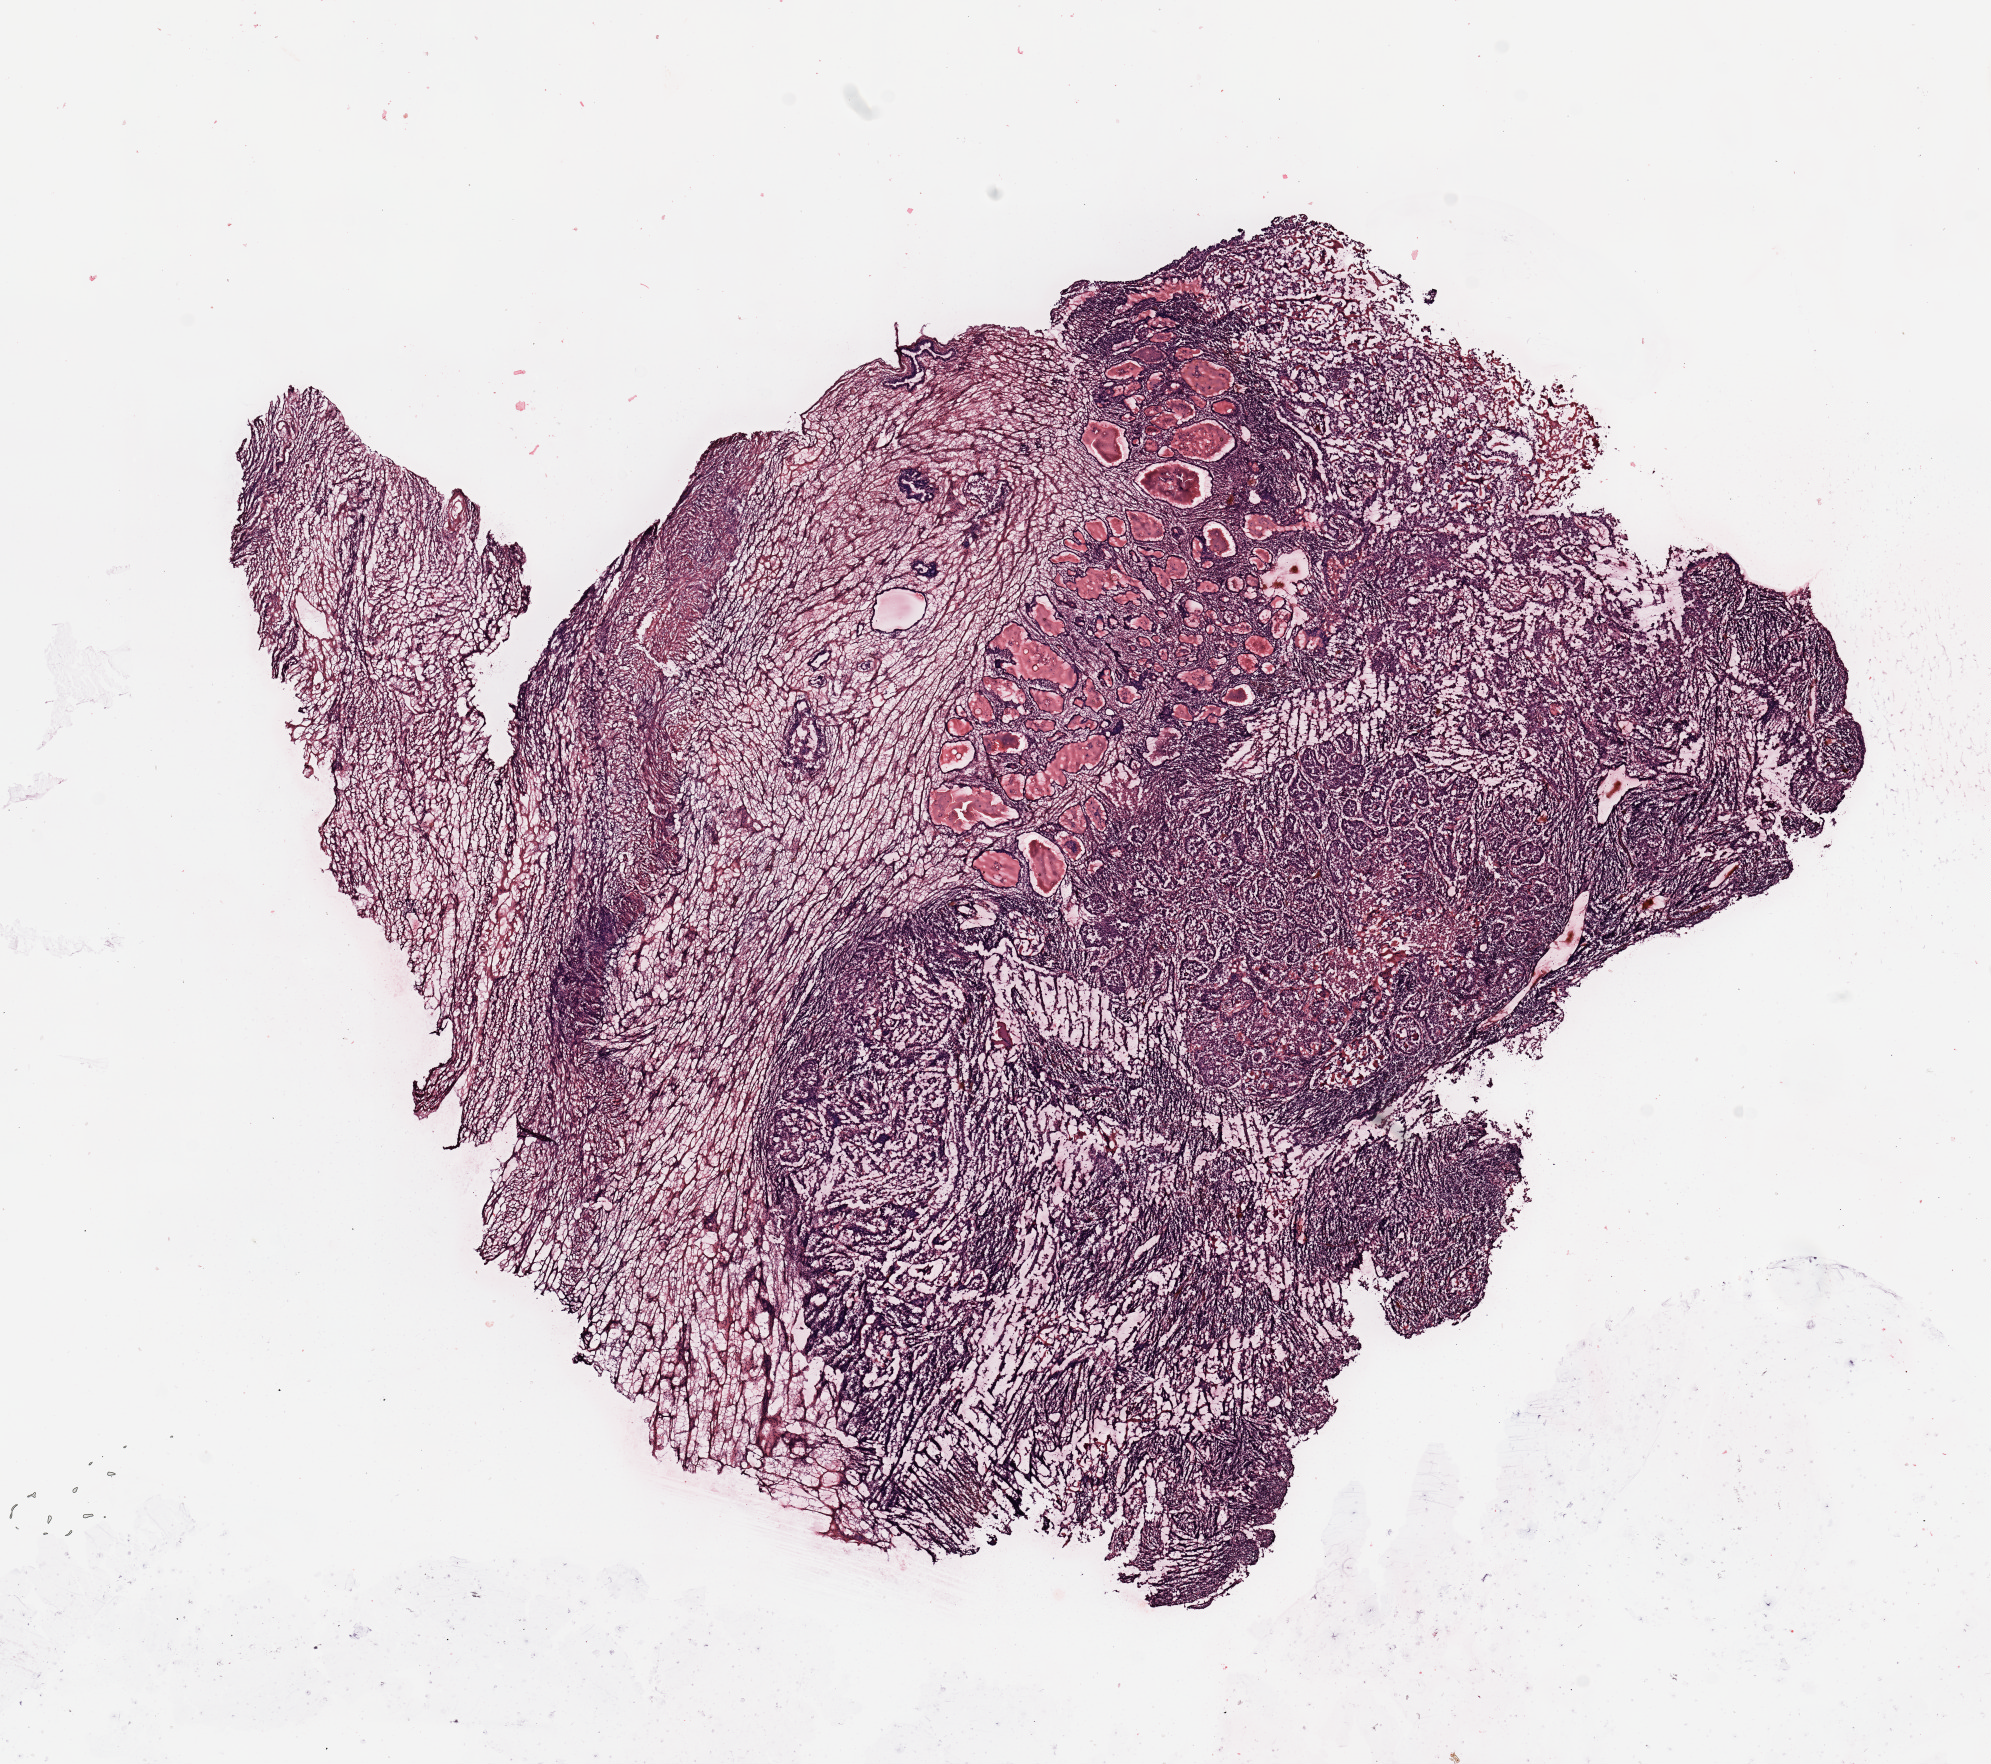
H&E-stained whole-slide image — shown as a low-resolution overview of the whole scanned area (about 15.8 x 14.0 mm, slide scanned at 20x). Tumour tissue sample, uterus. Patient: female, age 75 years. Histologic grade: G3 (poorly differentiated).
Histologic diagnosis: Endometrioid adenocarcinoma, NOS. AJCC pathologic stage: I.